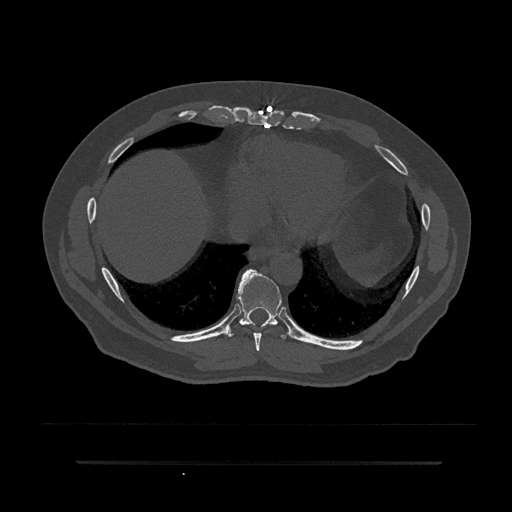
CT including the spine, one axial slice. Position 397 of 797 along the scan axis. Reconstruction kernel Br40s/3. Bone window (W 1800 / L 400 HU). 0.5 mm slice thickness. 512 × 512 image matrix. Patient: male, 59 years. From the clinical record (not read from this slice): primary cancer: bile ducts; vertebrae with lytic lesions (as recorded): T10.
Outlined on this slice (semi-automatically segmented with operator editing):
- T8 vertebra: bounding box [x1, y1, x2, y2] px = [253, 333, 262, 351]
- T9 vertebra: [226, 269, 286, 339]